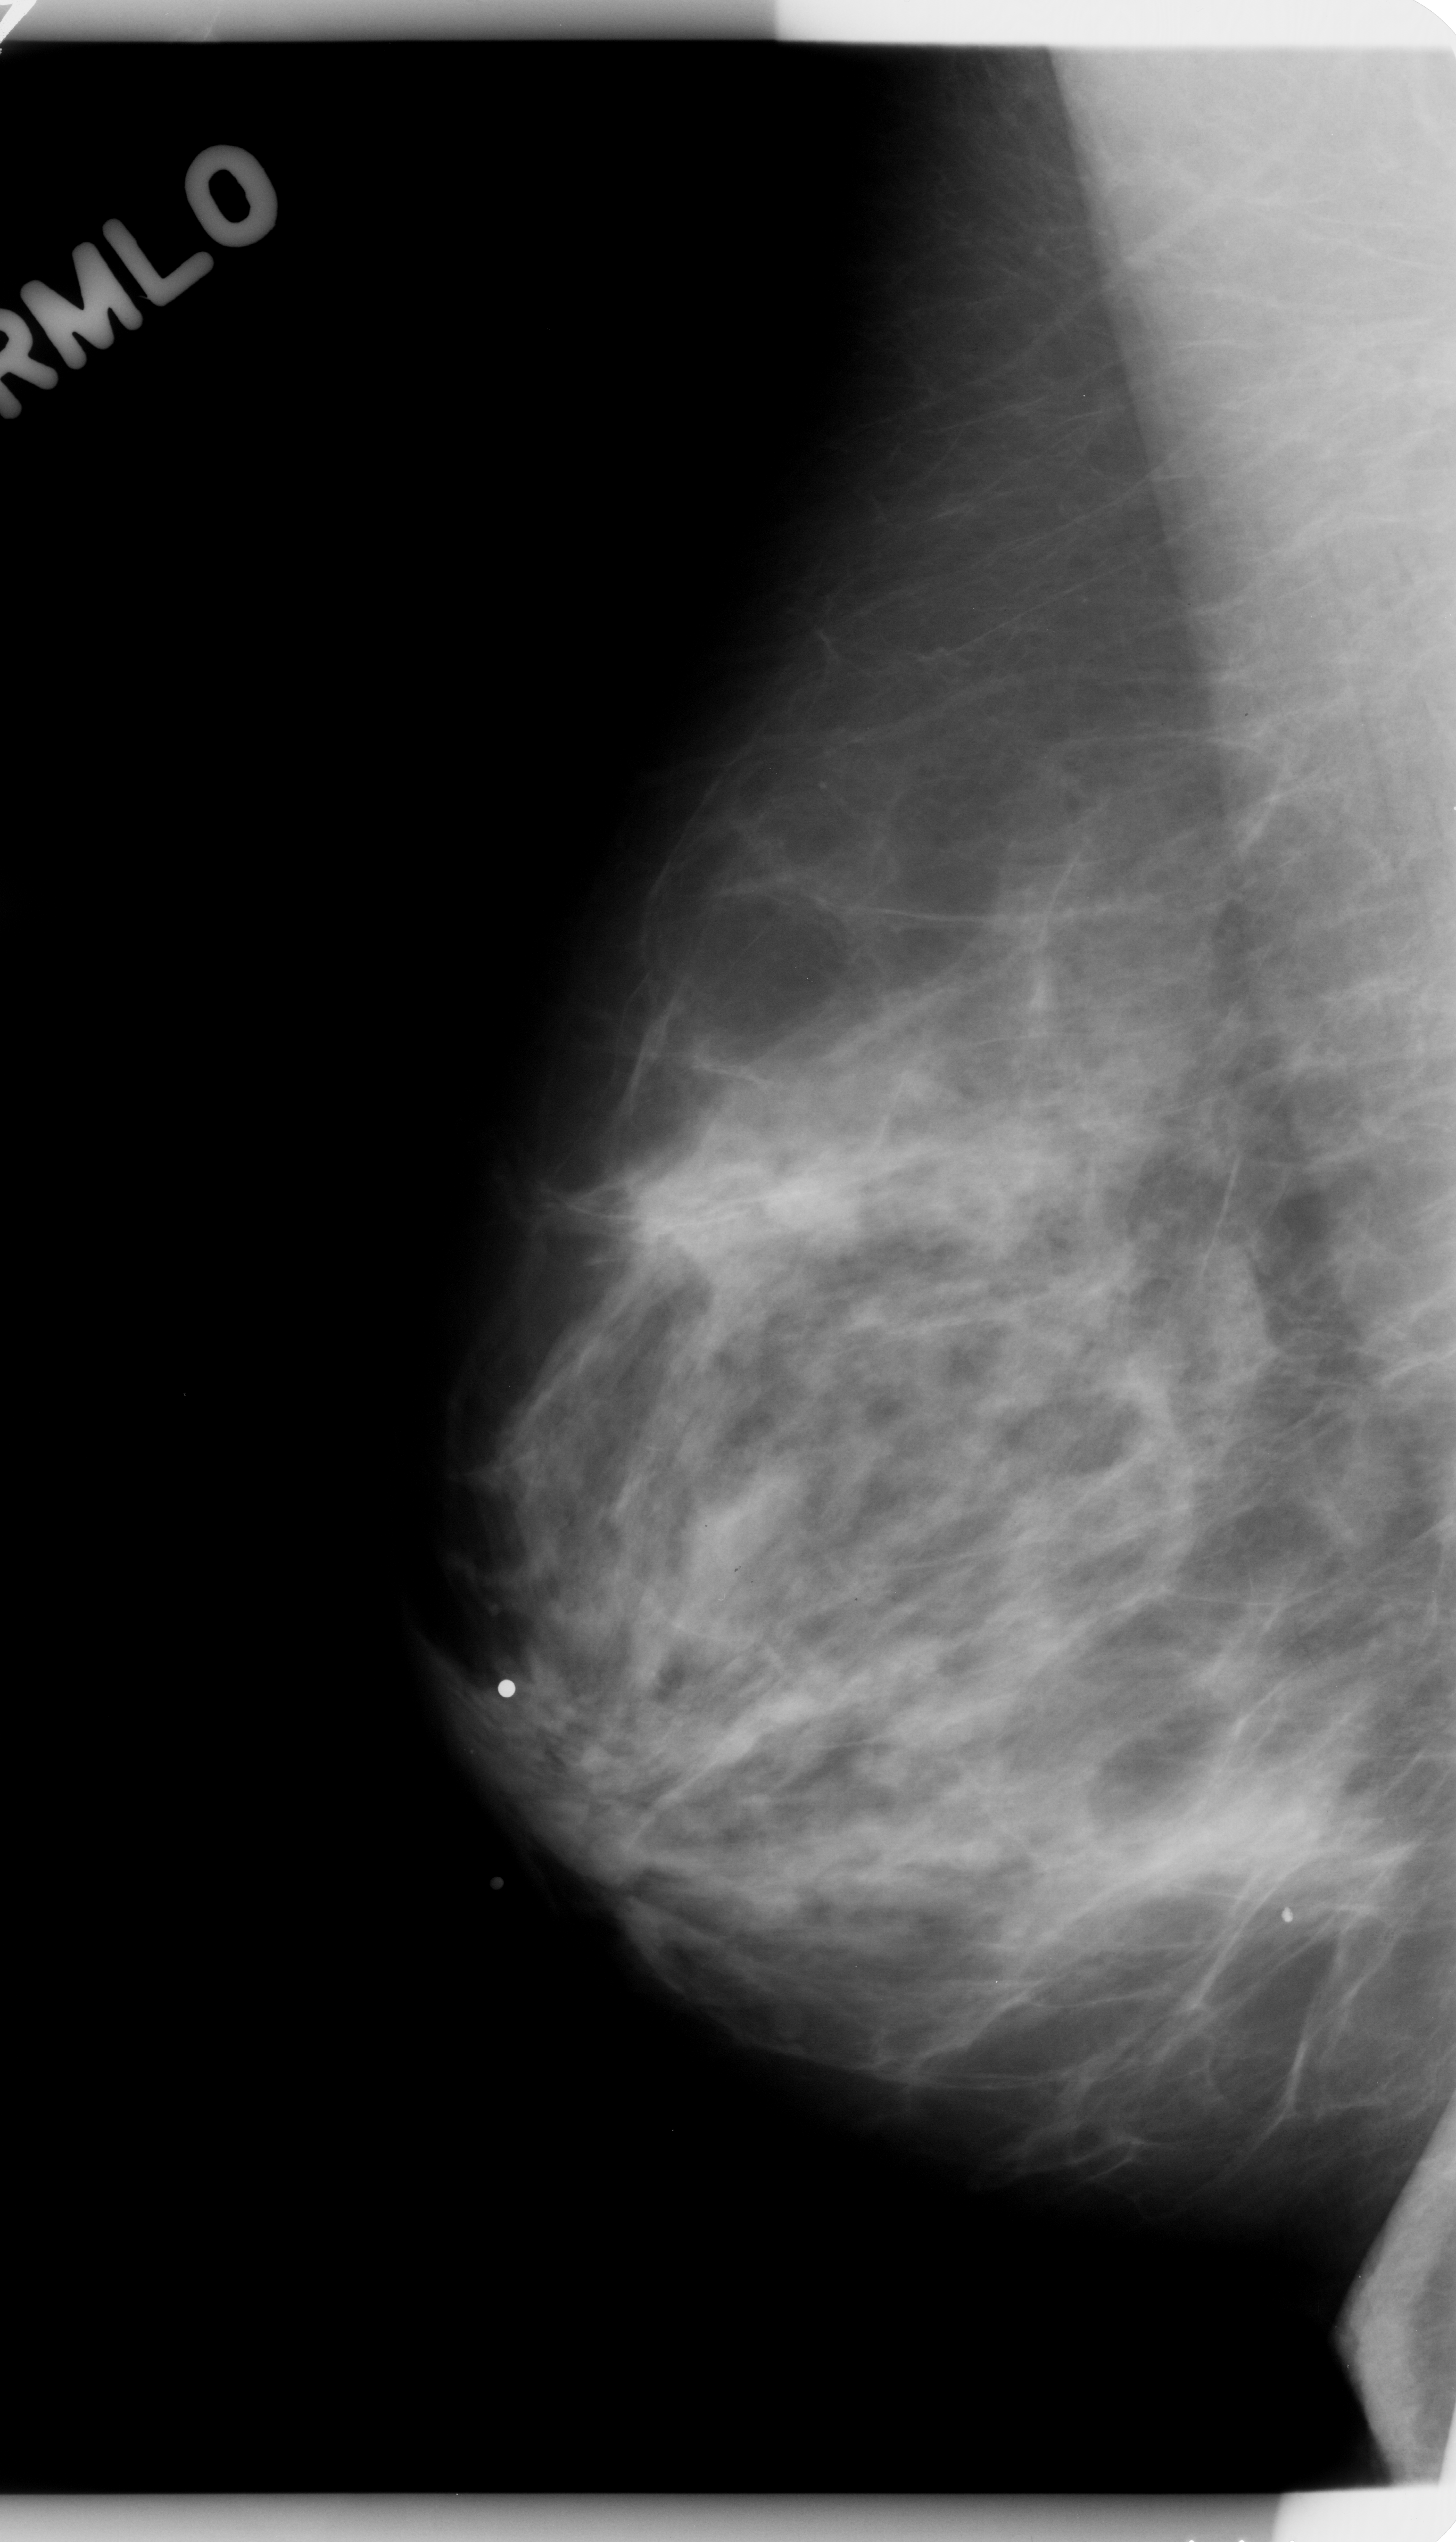
Mammogram (digitized film); right breast; MLO view; 1456 × 2542 image matrix.
Expert-marked regions of interest on this film, with their recorded descriptors:
- mass, shape oval, margins circumscribed; BI-RADS assessment category 4; pathology result (as recorded, not read from the image): benign: bounding box [x1, y1, x2, y2] px = [531, 1771, 675, 1898]